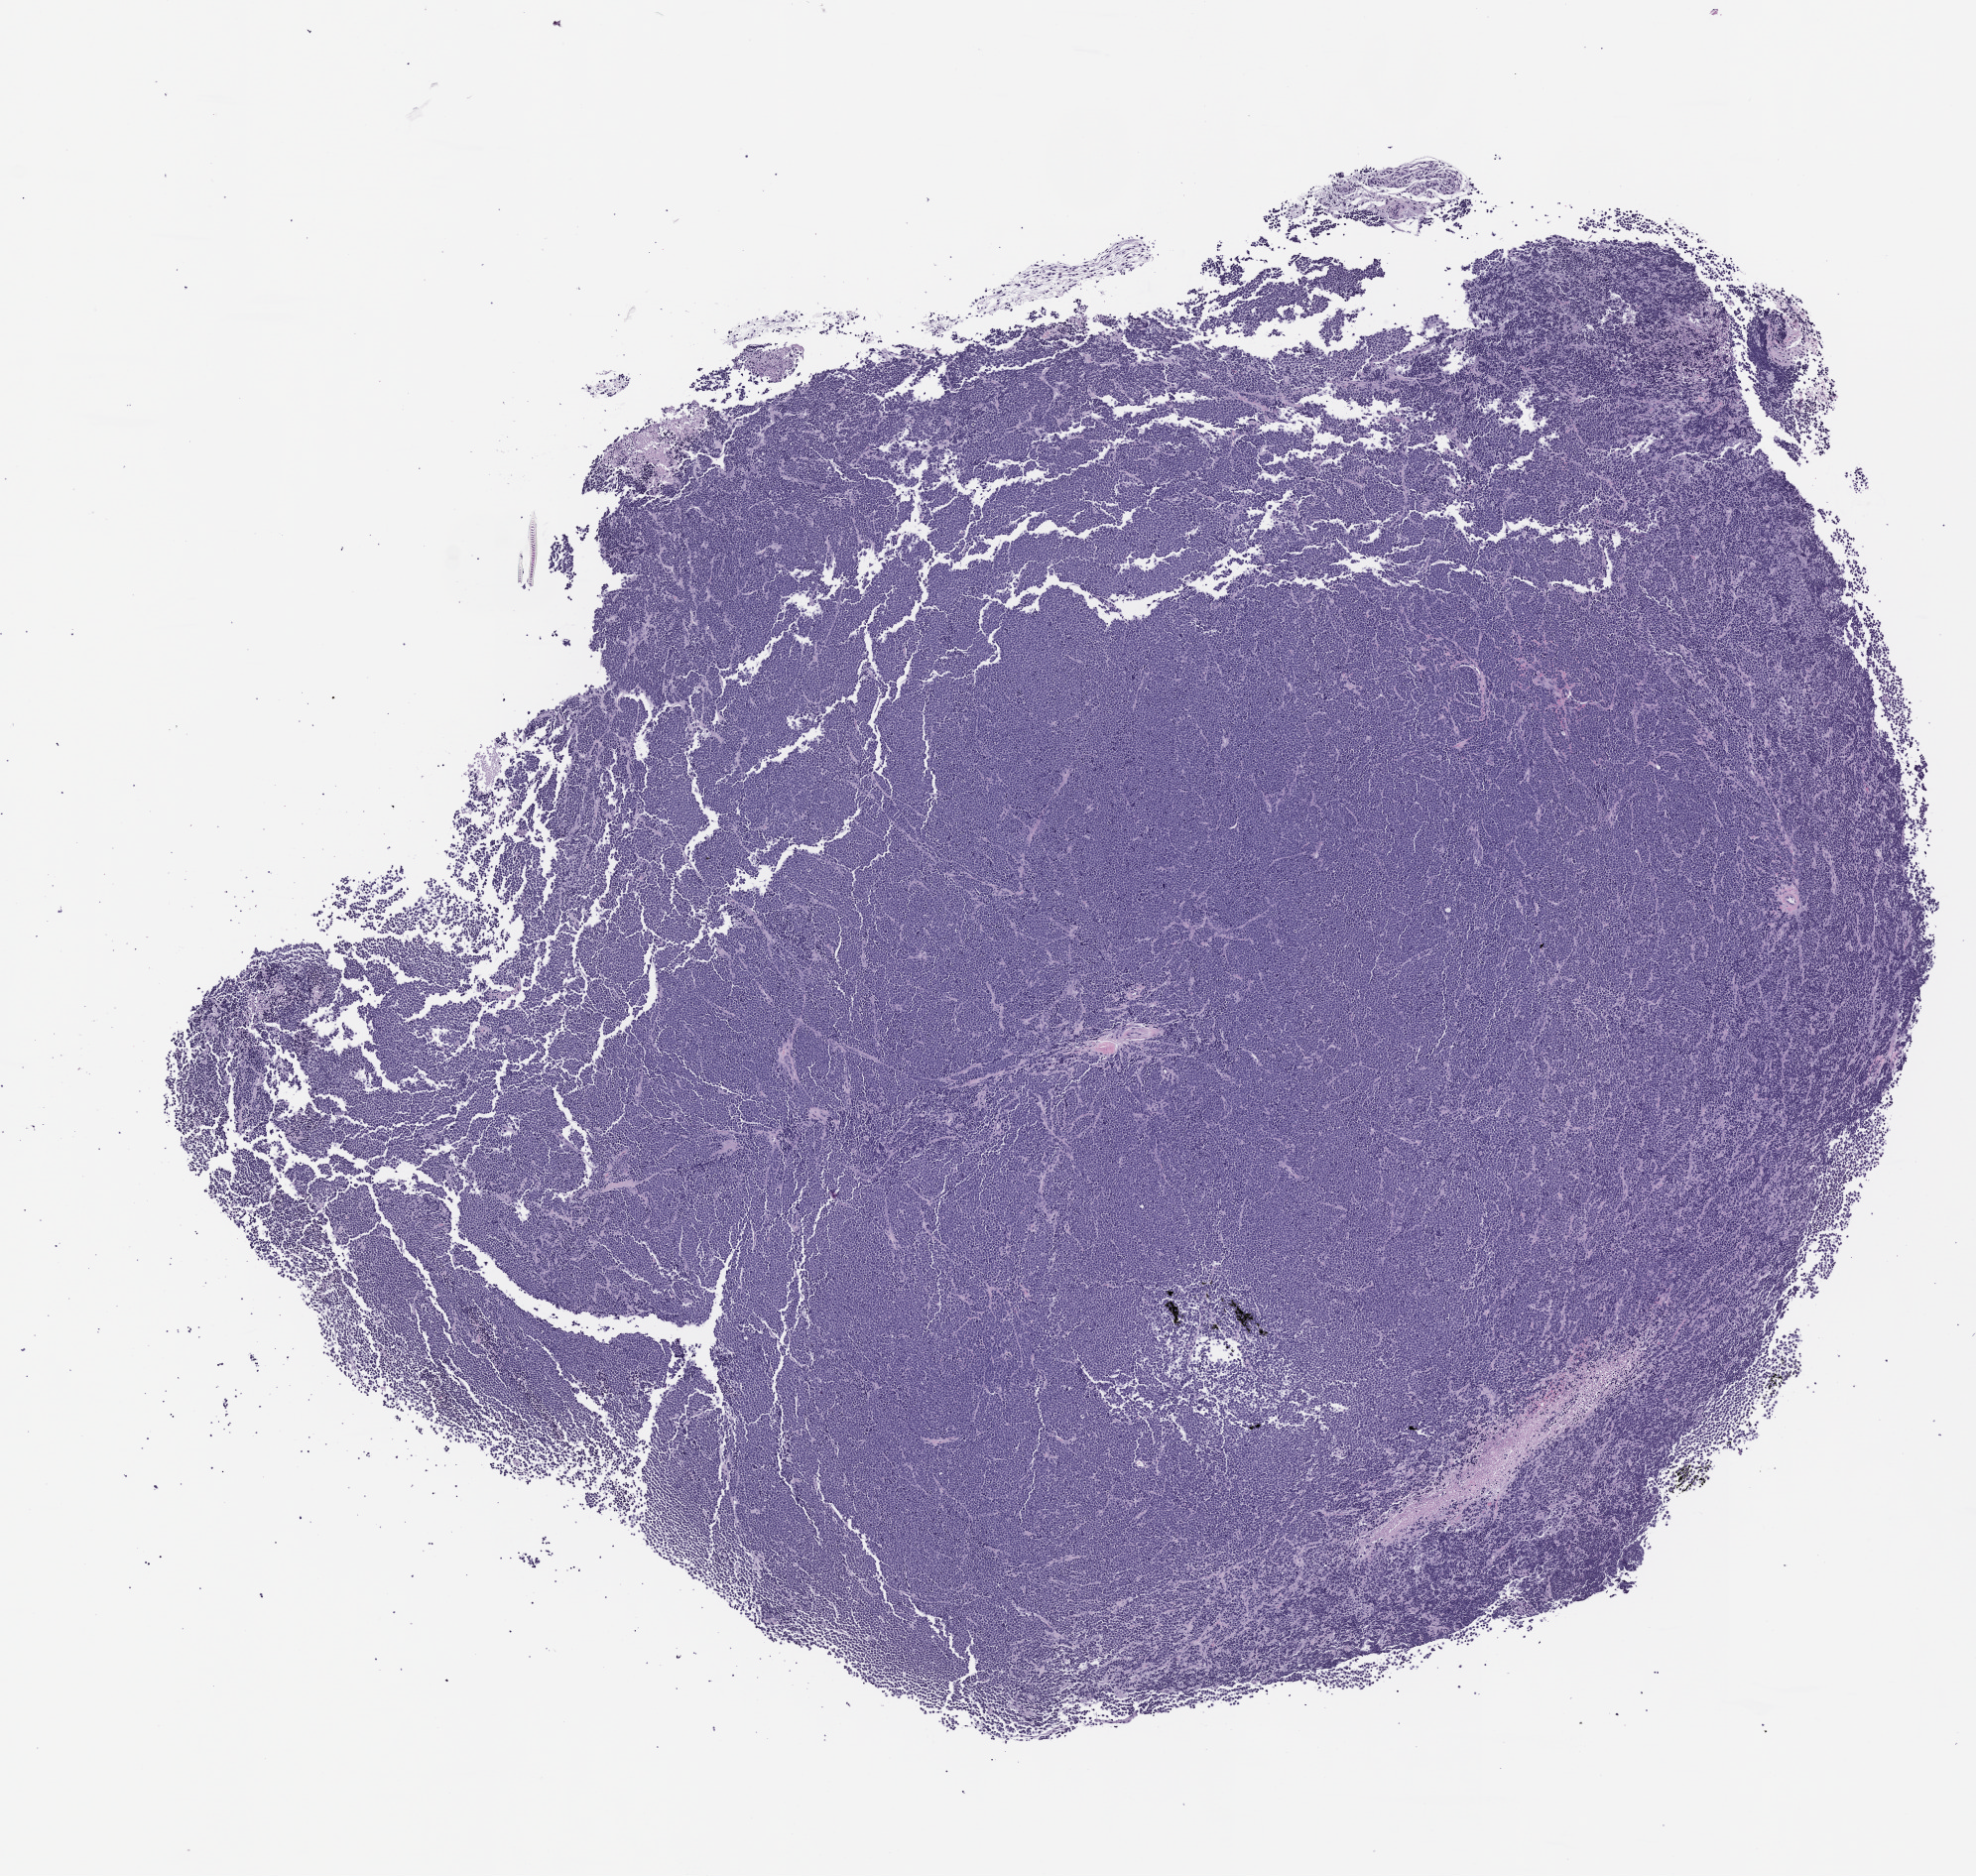
Hematoxylin and eosin (H&E) whole-slide image of a patient-derived xenograft (PDX) tumor grown in a mouse, passage 2 — a low-resolution overview of the entire scanned area, about 8.0 x 7.6 mm; FFPE section; originating tumor site category: lung.
Originating patient diagnosis: Lung Small Cell Carcinoma.